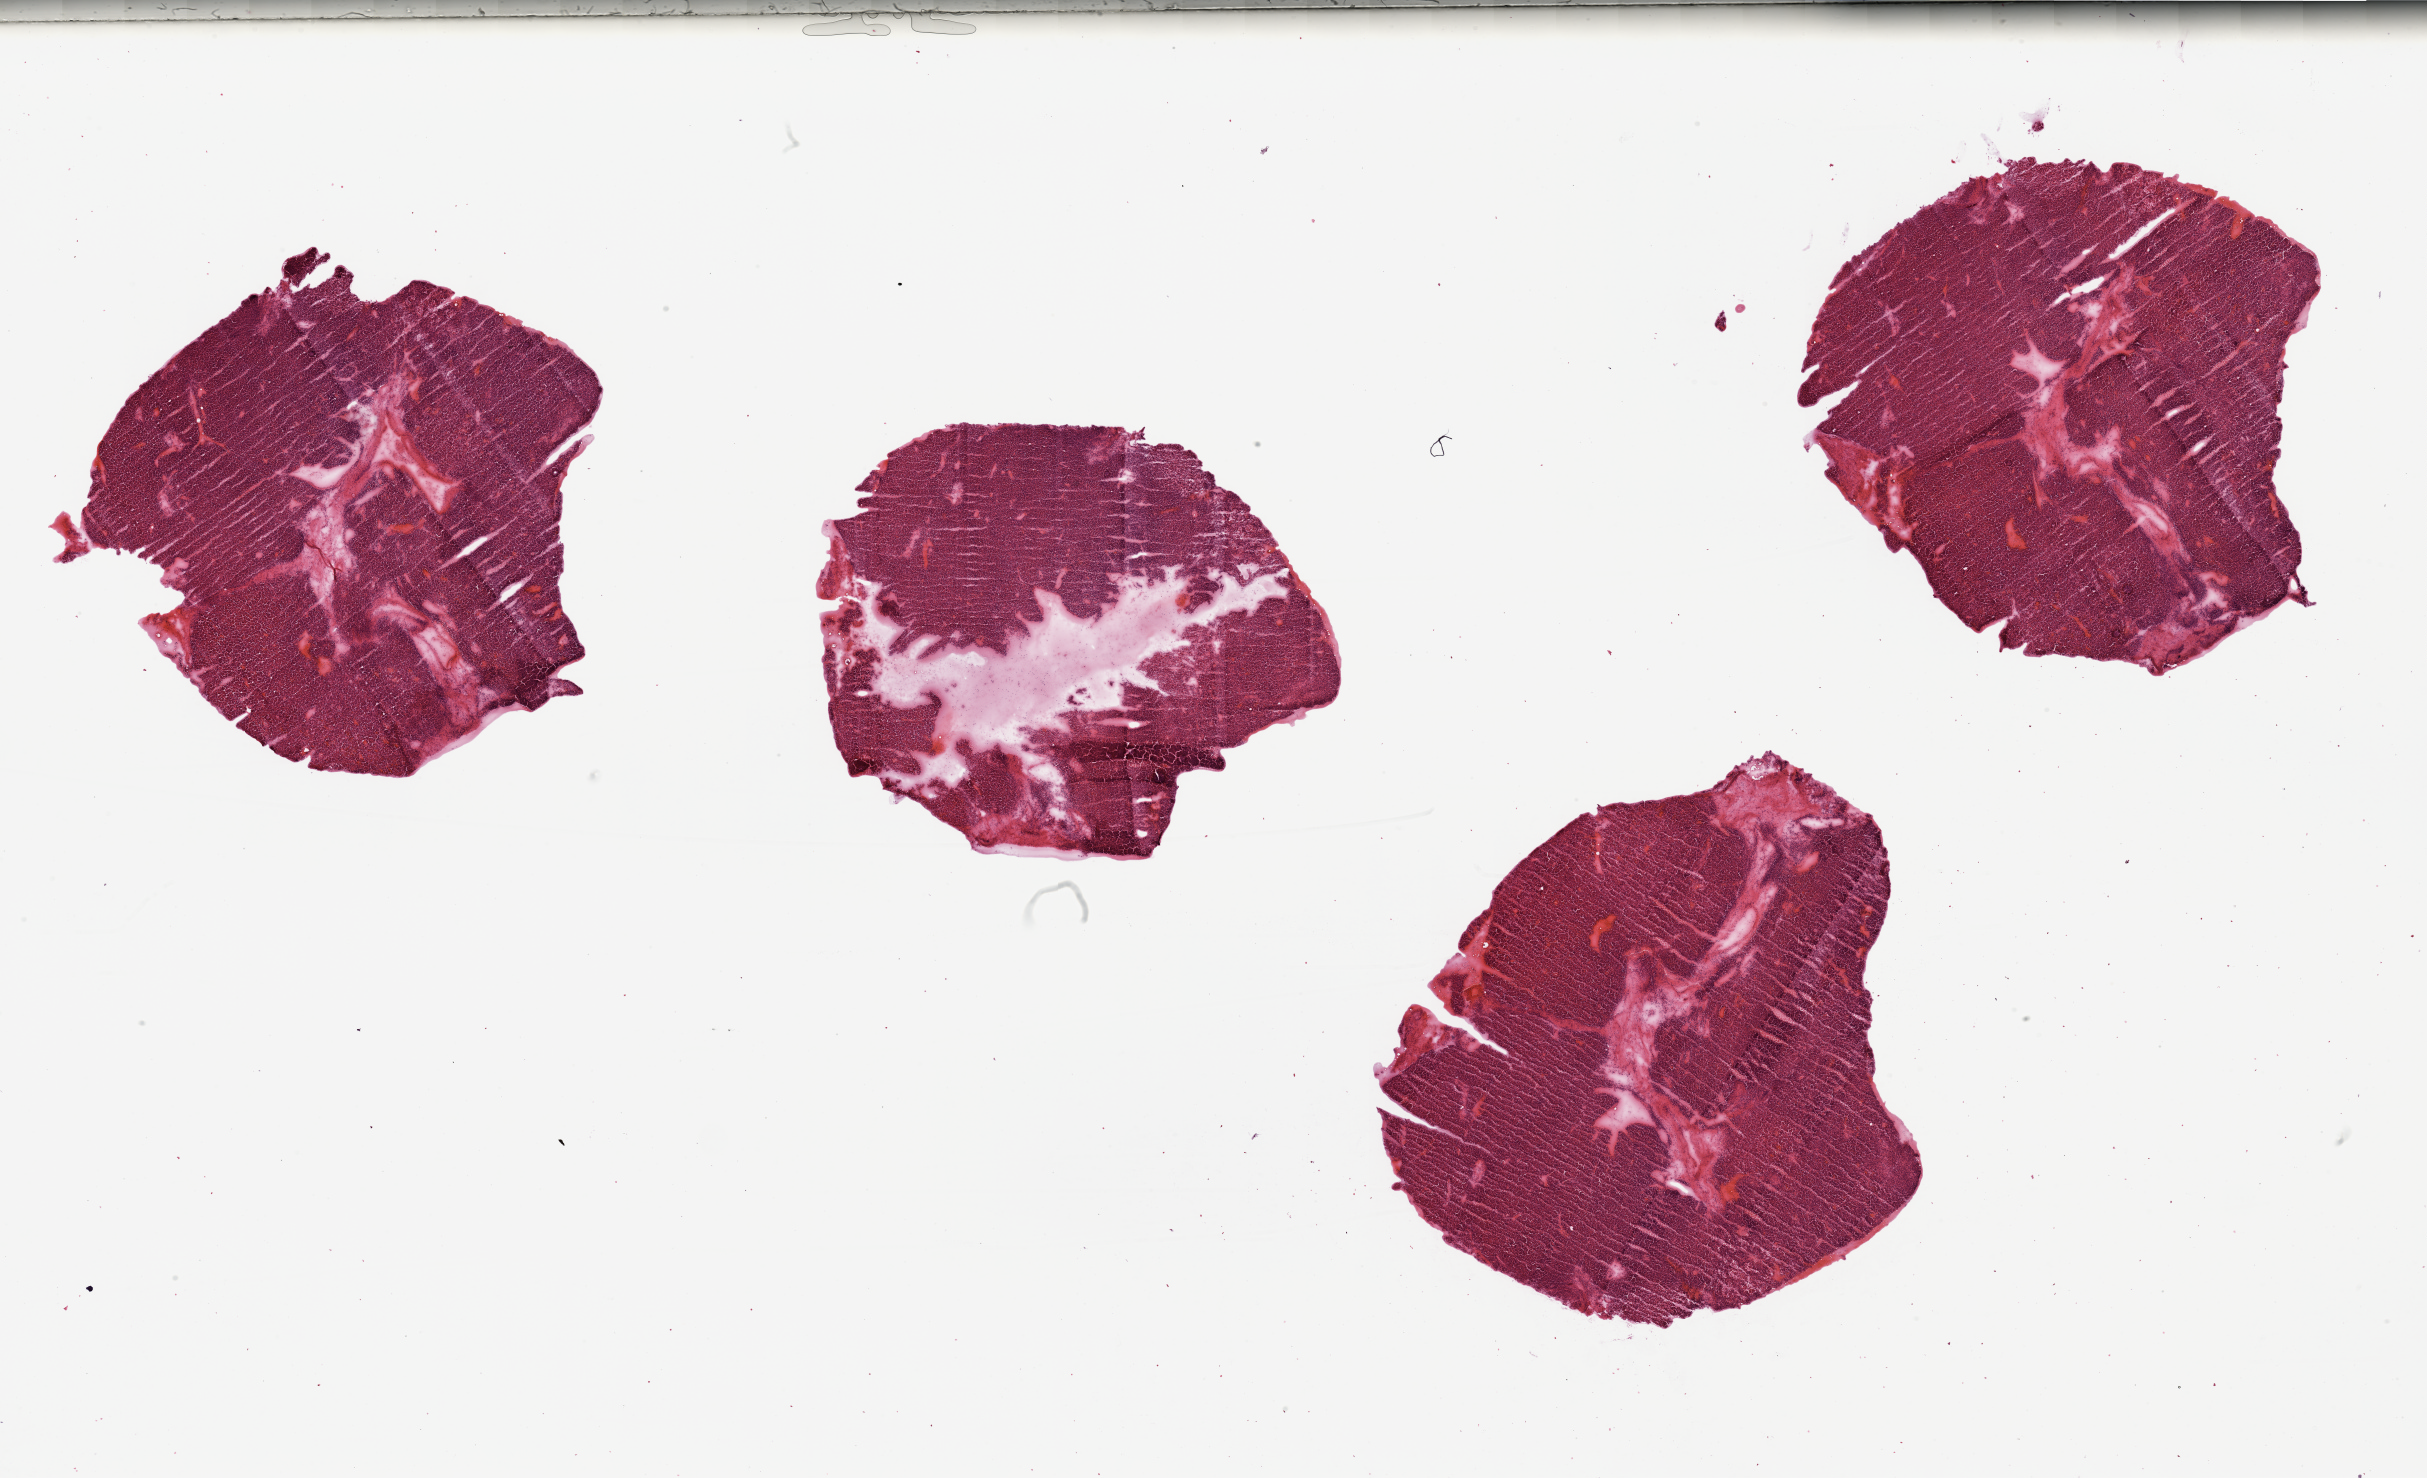
Digitized Hematoxylin and eosin (H&E) stained tissue section (whole slide), whole scanned area (about 38.4 x 23.4 mm) shown as a low-resolution overview. Tumour tissue sample, sampled site: kidney. Male, 67 y/o. Histologic grade: G2 (moderately differentiated). Pathologist review of this section (percent, as recorded): tumour nuclei 90%, necrosis 5%.
Histologic diagnosis: Renal cell carcinoma, NOS. AJCC pathologic stage: III. Primary tumour site (as recorded): middle.